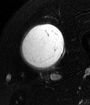
MRI of an extremity soft-tissue mass, one axial slice; T2-weighted fat-saturated; MR volume resampled by the dataset authors to the PET/CT grid (not the native acquisition matrix); 90 × 105 image matrix. Male patient. From the clinical record (not read from this slice): histological type: mixoid liposarcoma; grade: low; site of the primary tumour: left thigh.
Structures marked on this image (expert contour drawn on MRI and transferred to this co-registered scan by the dataset authors):
- gross tumour volume (mass): bounding box <20,25,63,70> (left, top, right, bottom; pixels)